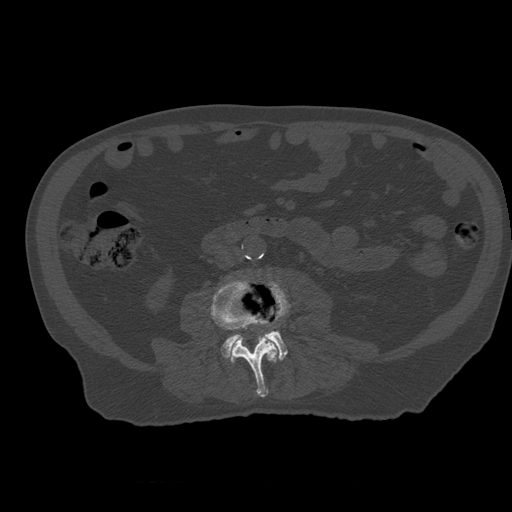
CT including the spine, one axial slice; position 180 of 399 along the scan axis; 120 kVp; bone window (W 1800 / L 400 HU); 1.25 mm slice thickness; 512 × 512 image matrix, field of view 407 × 407 mm. Patient age 73 years. From the clinical record (not read from this slice): primary cancer: prostate.
Annotated regions visible in this slice (semi-automatic segmentation, software-assisted and operator-edited):
- L3 vertebra: bounding box [x1, y1, x2, y2] px = [211, 280, 280, 398]
- L4 vertebra: [221, 282, 288, 360]